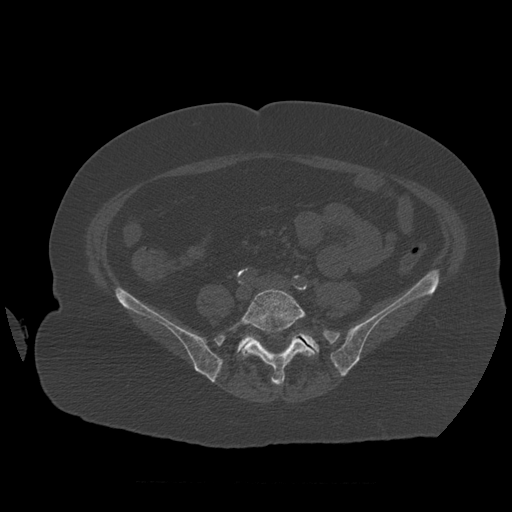
CT including the spine, one axial slice. Slice 180 of 399 in the series (ordered by position). Reconstruction kernel STANDARD. Bone window (W 1800 / L 400 HU). 1.25 mm slice thickness. 512 × 512 image matrix, field of view 404 × 404 mm. Patient age 81 years. Case-level facts recorded for this patient, not image findings: primary cancer: renal.
Structures marked on this image (semi-automatic segmentation, software-assisted and operator-edited):
- L5 vertebra: bounding box [x1, y1, x2, y2] px = [229, 289, 316, 386]